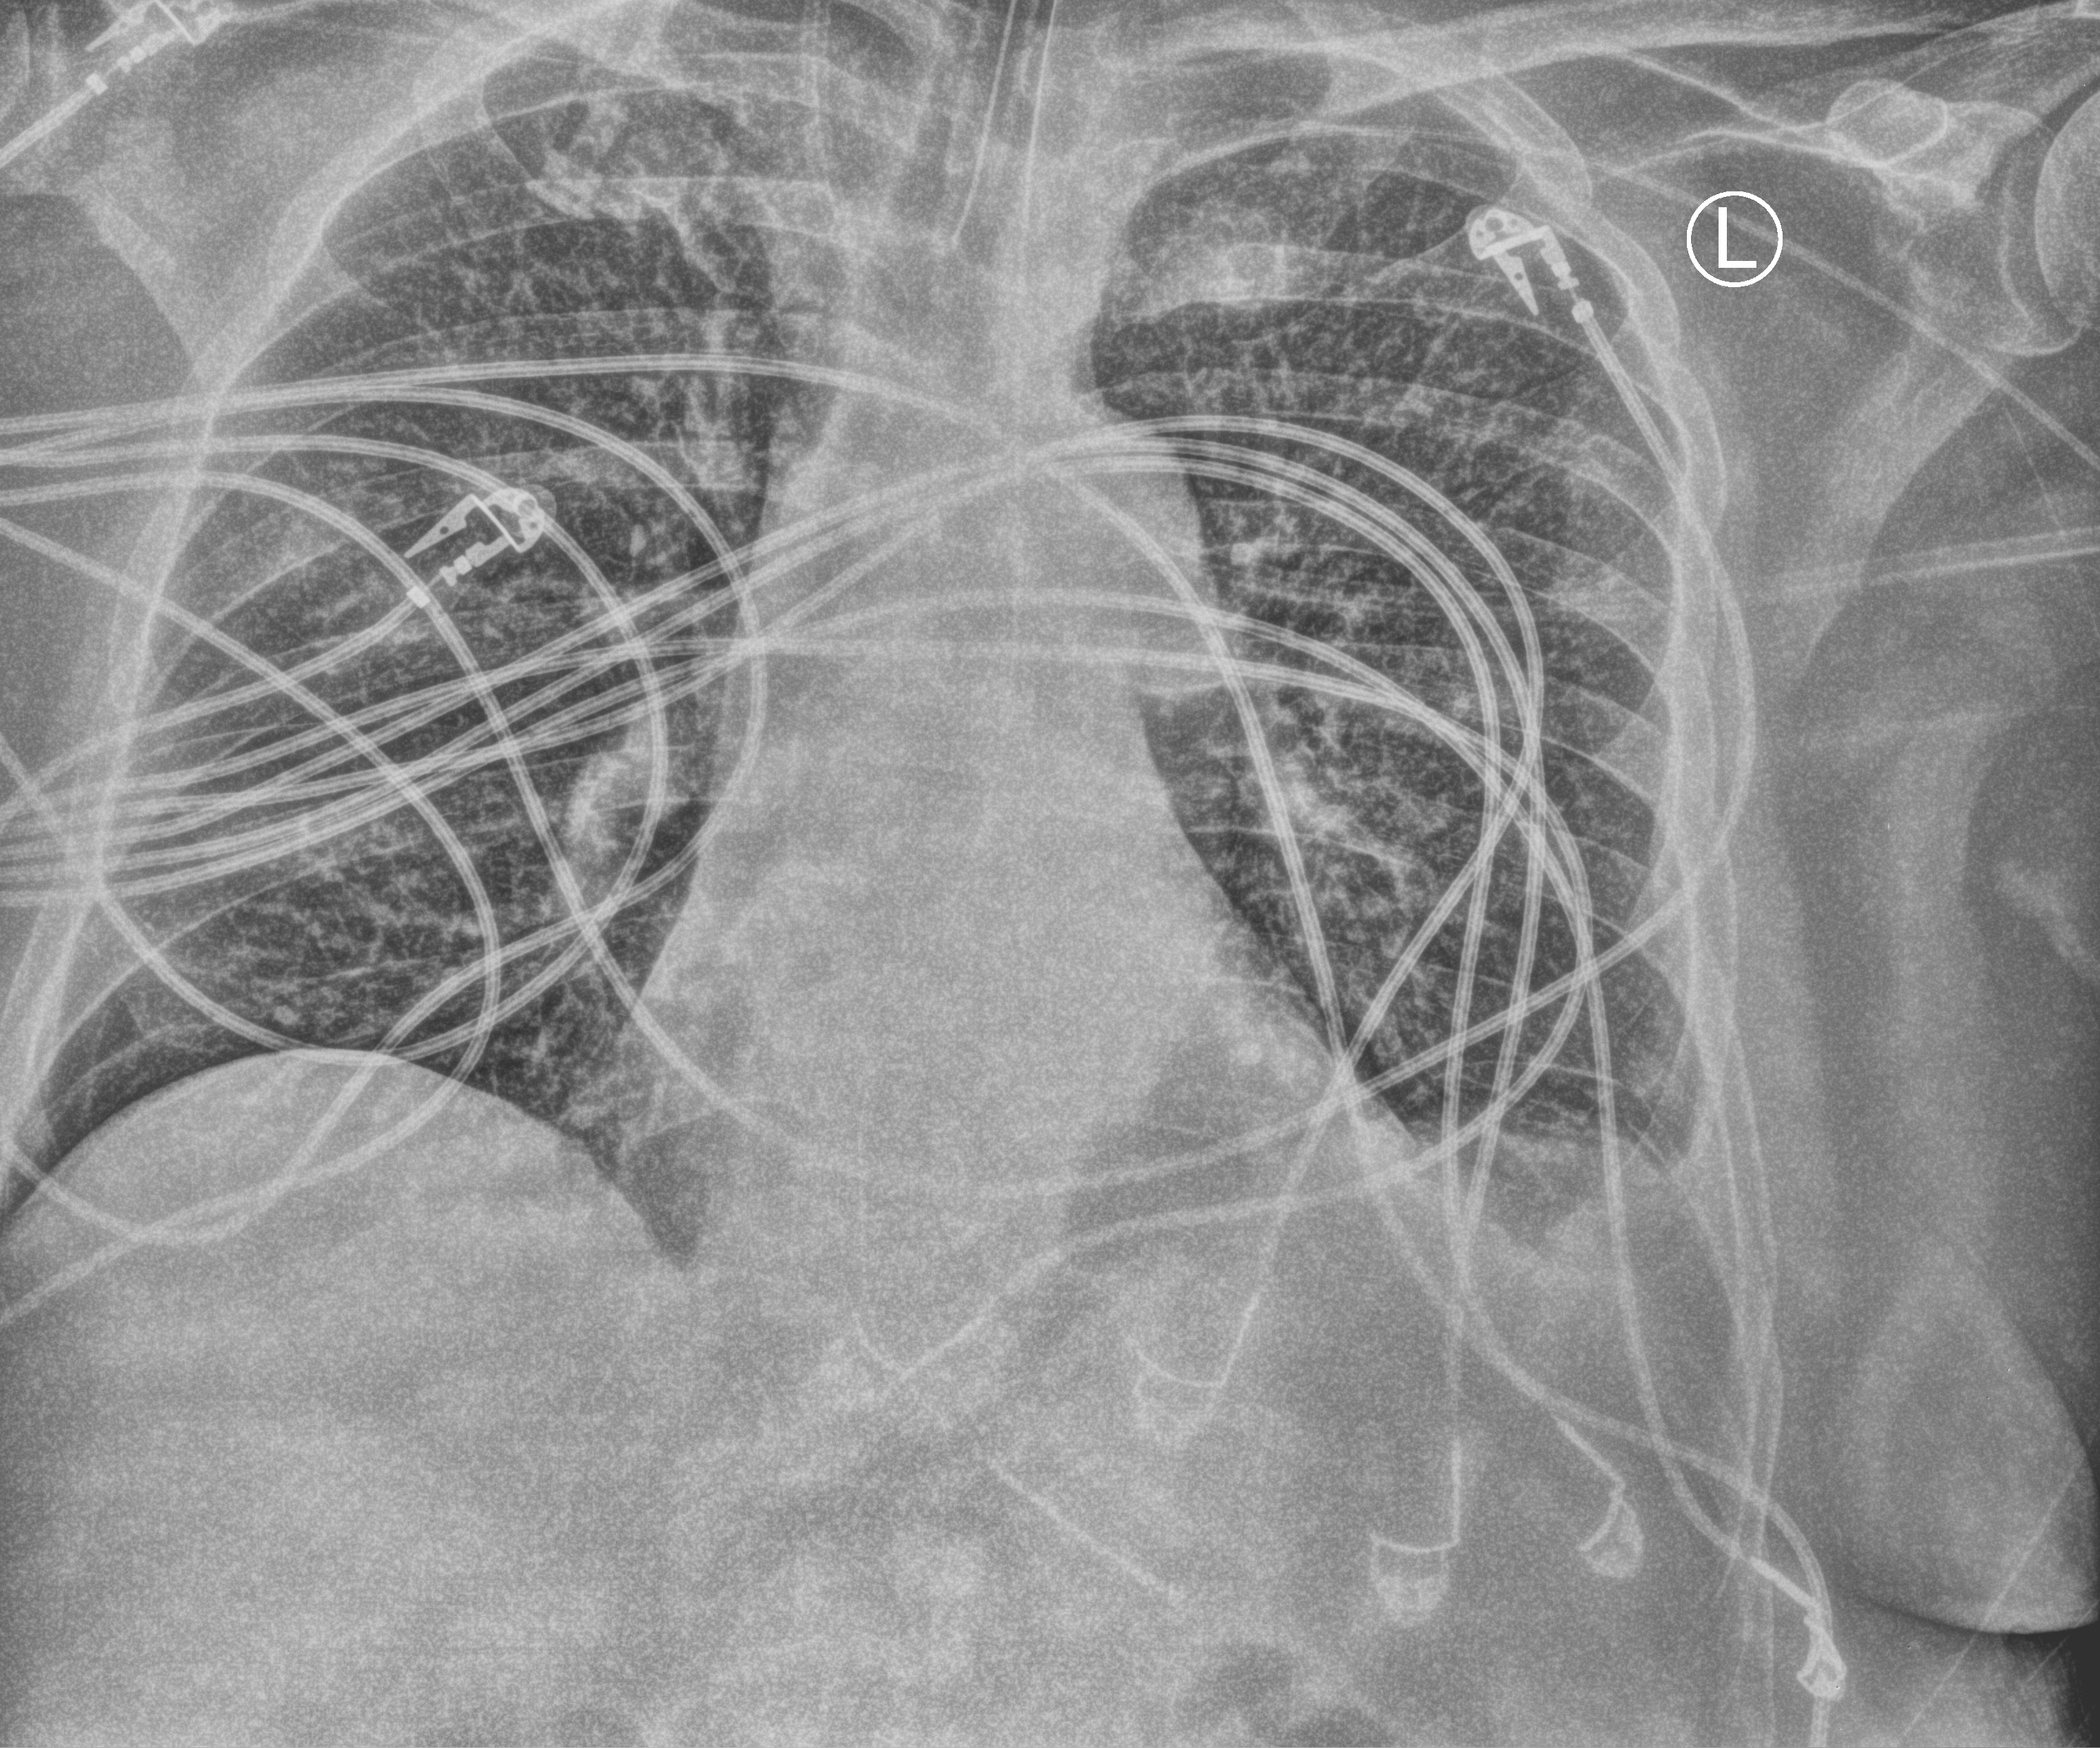
Chest X-ray (portable). Male patient hospitalised with COVID-19, age 60–74 years.
From the hospital-stay record, not from the radiograph (when in the stay this image was taken is not recorded):
- length of hospital stay: 22 days
- mechanically ventilated during this hospital stay: yes
- COPD (admission record): no